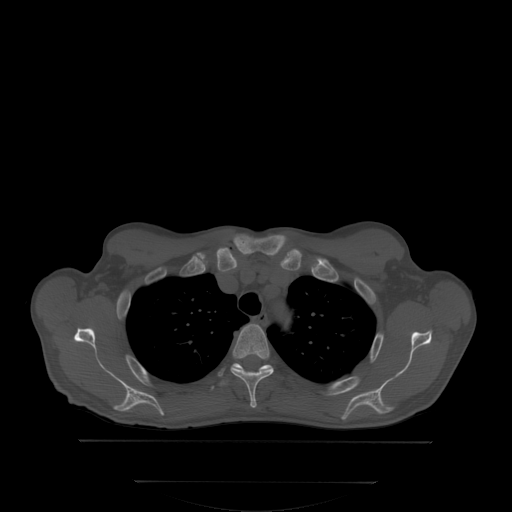
CT including the spine, one axial slice; bone window (W 1800 / L 400 HU); 2.5 mm slice thickness; 512 × 512 image matrix, field of view 500 × 500 mm. Male patient, age 58 years. Case-level facts recorded for this patient, not image findings: primary cancer: prostate; vertebrae with lytic lesions (as recorded): L1.
Annotated regions visible in this slice (semi-automatic segmentation, software-assisted and operator-edited):
- T3 vertebra: bounding box [x1, y1, x2, y2] px = [231, 324, 272, 407]
- T4 vertebra: [233, 364, 273, 371]